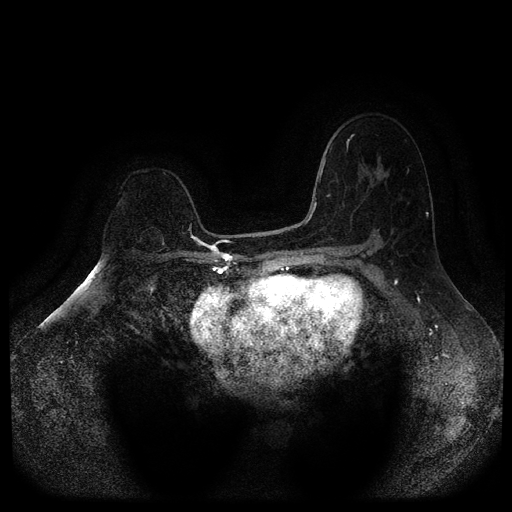
Breast MRI (dynamic contrast-enhanced, multi-phase), one axial slice. Slice 70 of 116 in the series (ordered by position). Dynamic contrast-enhanced series, time point 2 of 5 at this slice position (early post-contrast). 1.5 T. TE 2.6 ms, TR 5.4 ms. 512 × 512 image matrix, field of view 340 × 340 mm. Female patient, age 64 years.
Outlined on this slice (semi-automatically segmented with operator editing):
- breast lesion (labelled benign in the annotation): bounding box <136,227,165,246> (left, top, right, bottom; pixels)